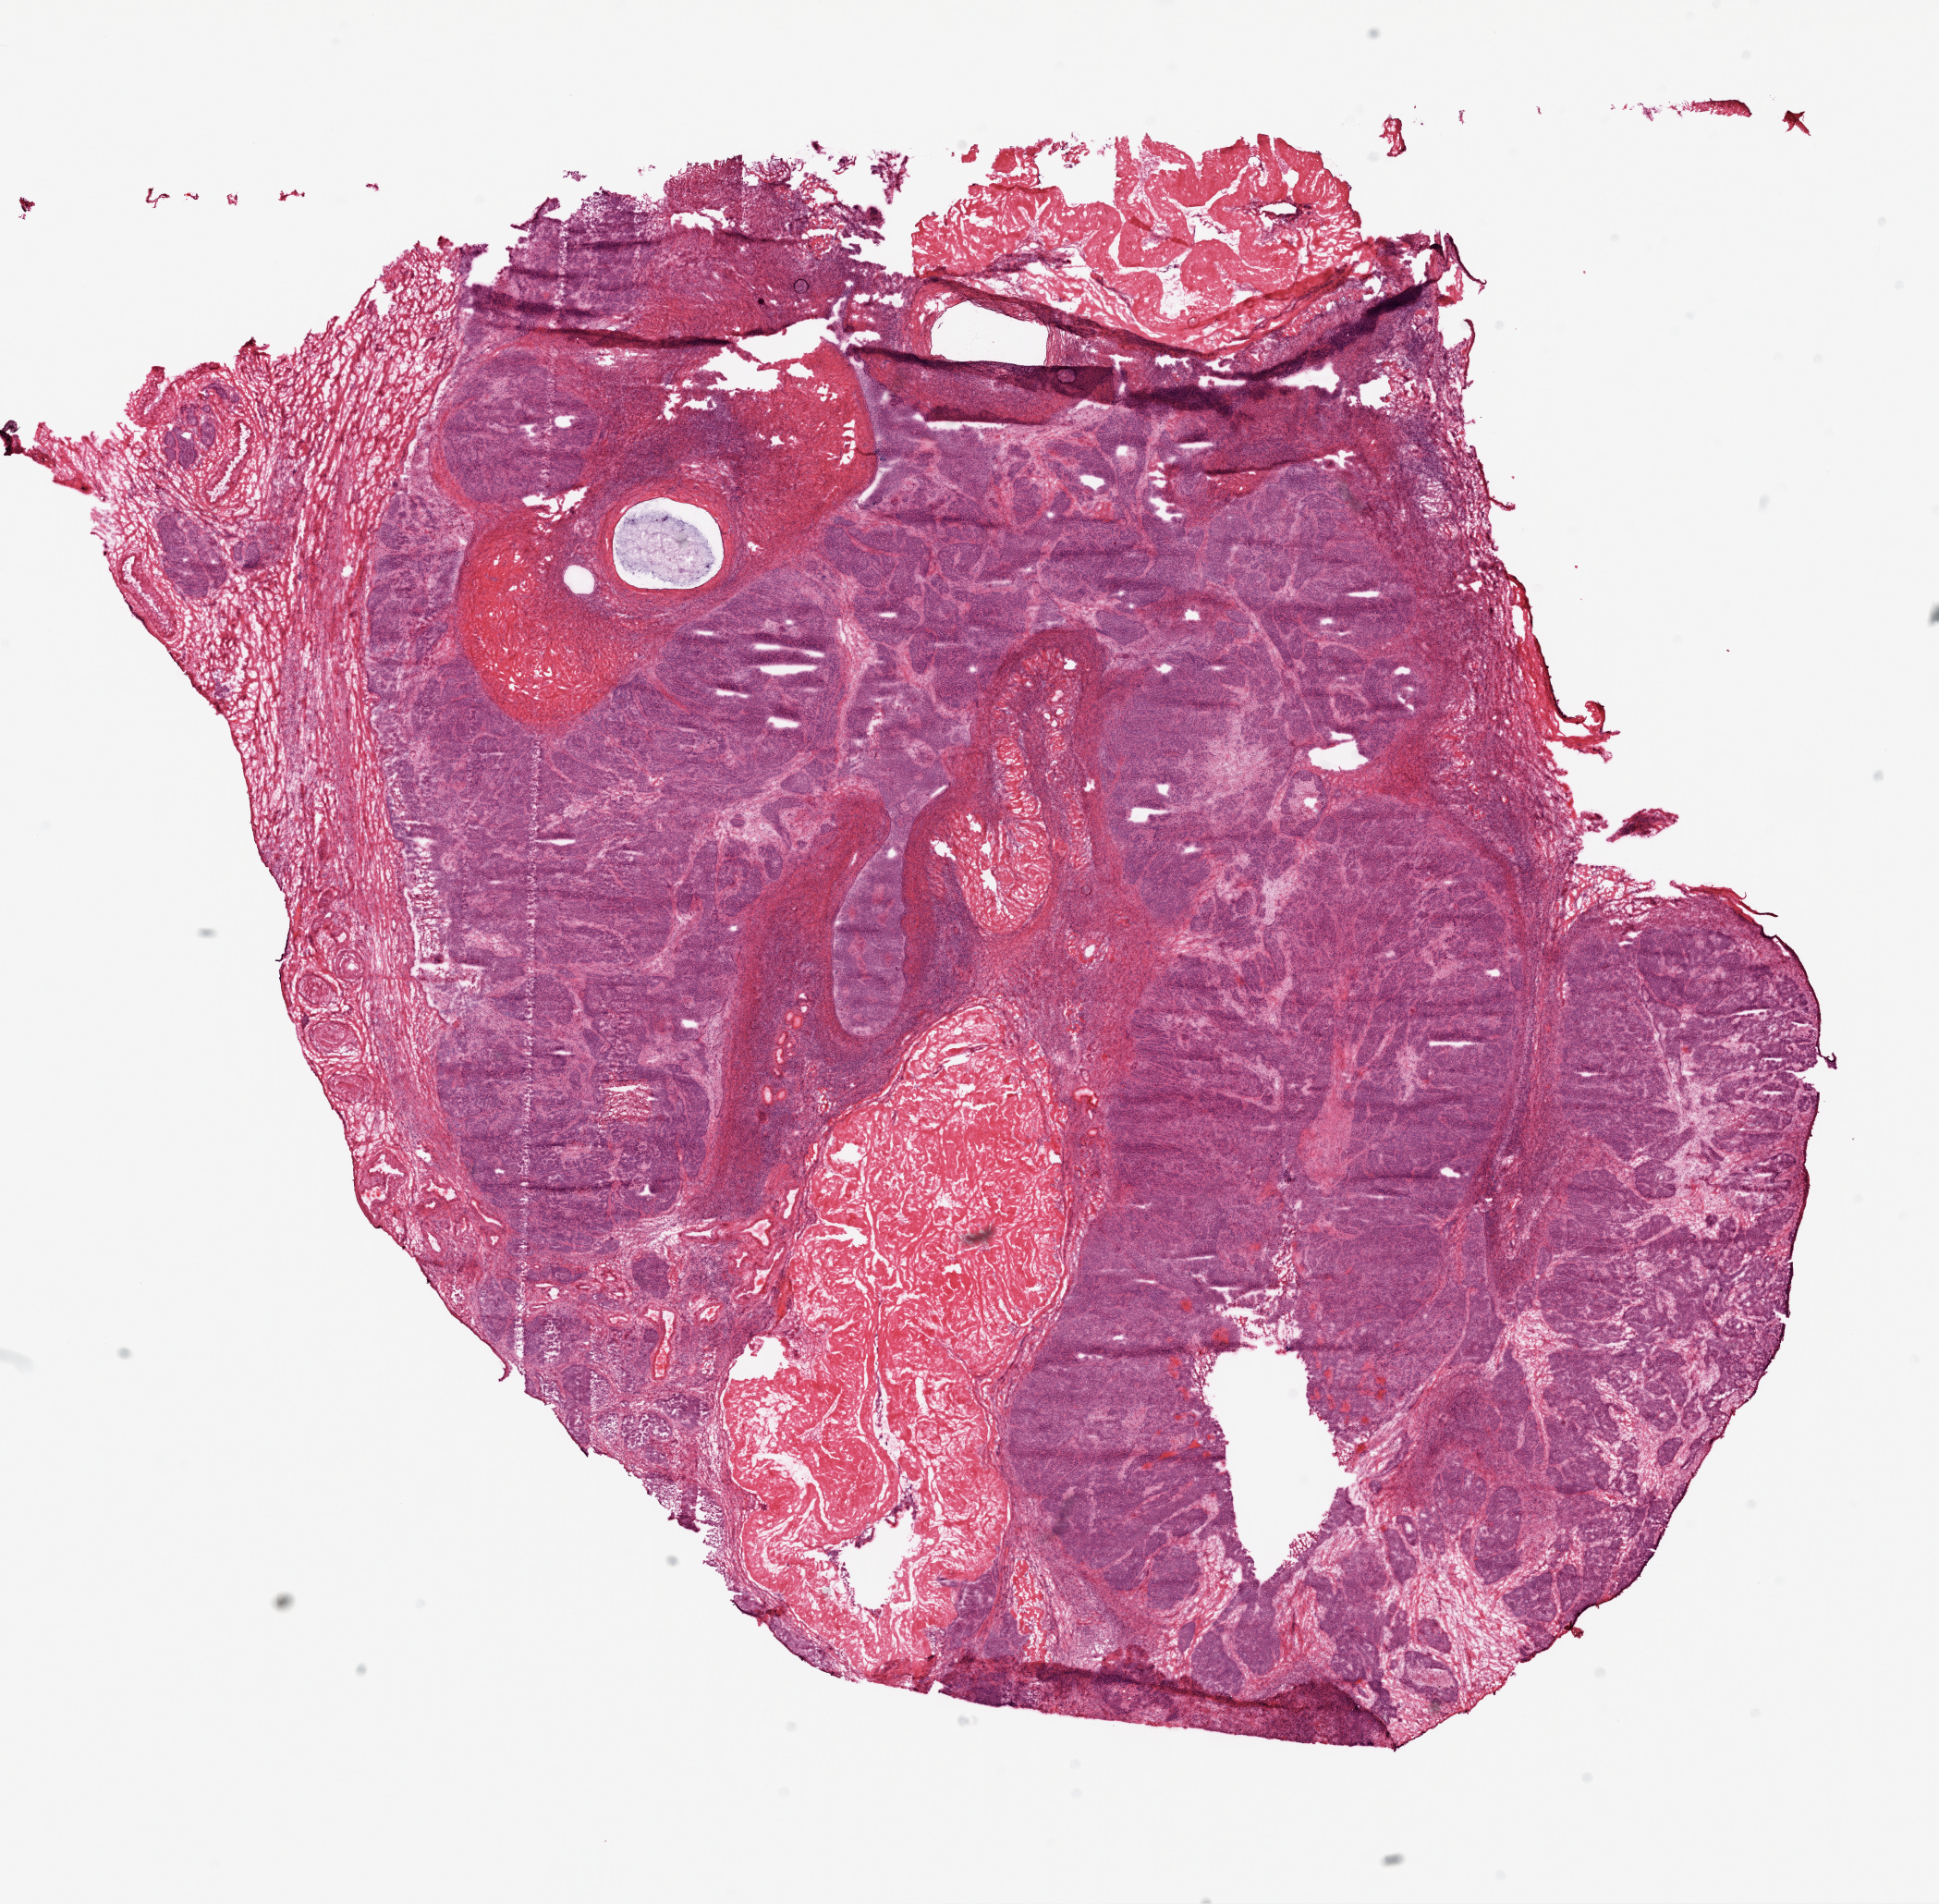
Whole-slide histology image, H&E-stained, a low-resolution overview of the entire scanned area, about 16.9 x 16.6 mm, frozen section from the top of the tissue portion, ovary, primary tumour sample. Patient: female, age at initial diagnosis 62 years. Histologic grade: G3 (poorly differentiated). Slide review estimates, as recorded: tumour cells 75%, tumour nuclei 95%, stromal cells 10%, necrosis 15%.
• laterality: bilateral
• FIGO stage: IV
• pathologic diagnosis: Serous cystadenocarcinoma, NOS